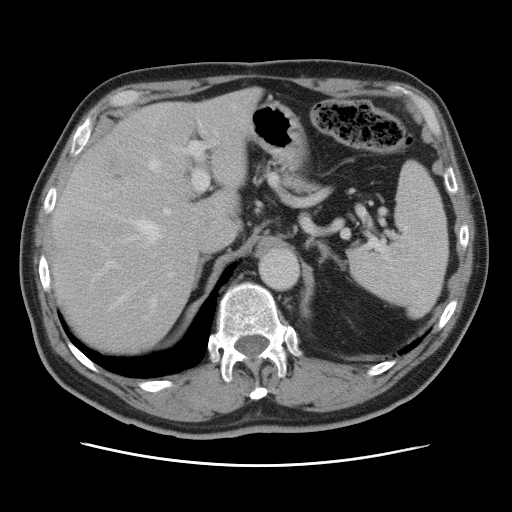
Contrast-enhanced abdominal CT, one axial slice. Slice 55 of 80 in the series (ordered by position). Intravenous contrast given. Soft-tissue window (W 400 / L 40 HU). 5 mm slice thickness. 512 × 512 image matrix, field of view 370 × 370 mm. Male patient, age 69 years. Case-level facts recorded for this patient, not image findings: diagnosis: colorectal cancer liver metastases, imaged before liver resection; multiple liver metastases: no.
Structures marked on this image (expert manual segmentation):
- hepatic veins: bounding box <116,125,203,306> (left, top, right, bottom; pixels)
- liver: <52,91,256,354>
- planned liver remnant (the part of the liver to remain after resection): <52,91,256,355>
- portal vein (with intrahepatic branches): <103,129,218,277>
- liver metastasis: <109,163,115,169>